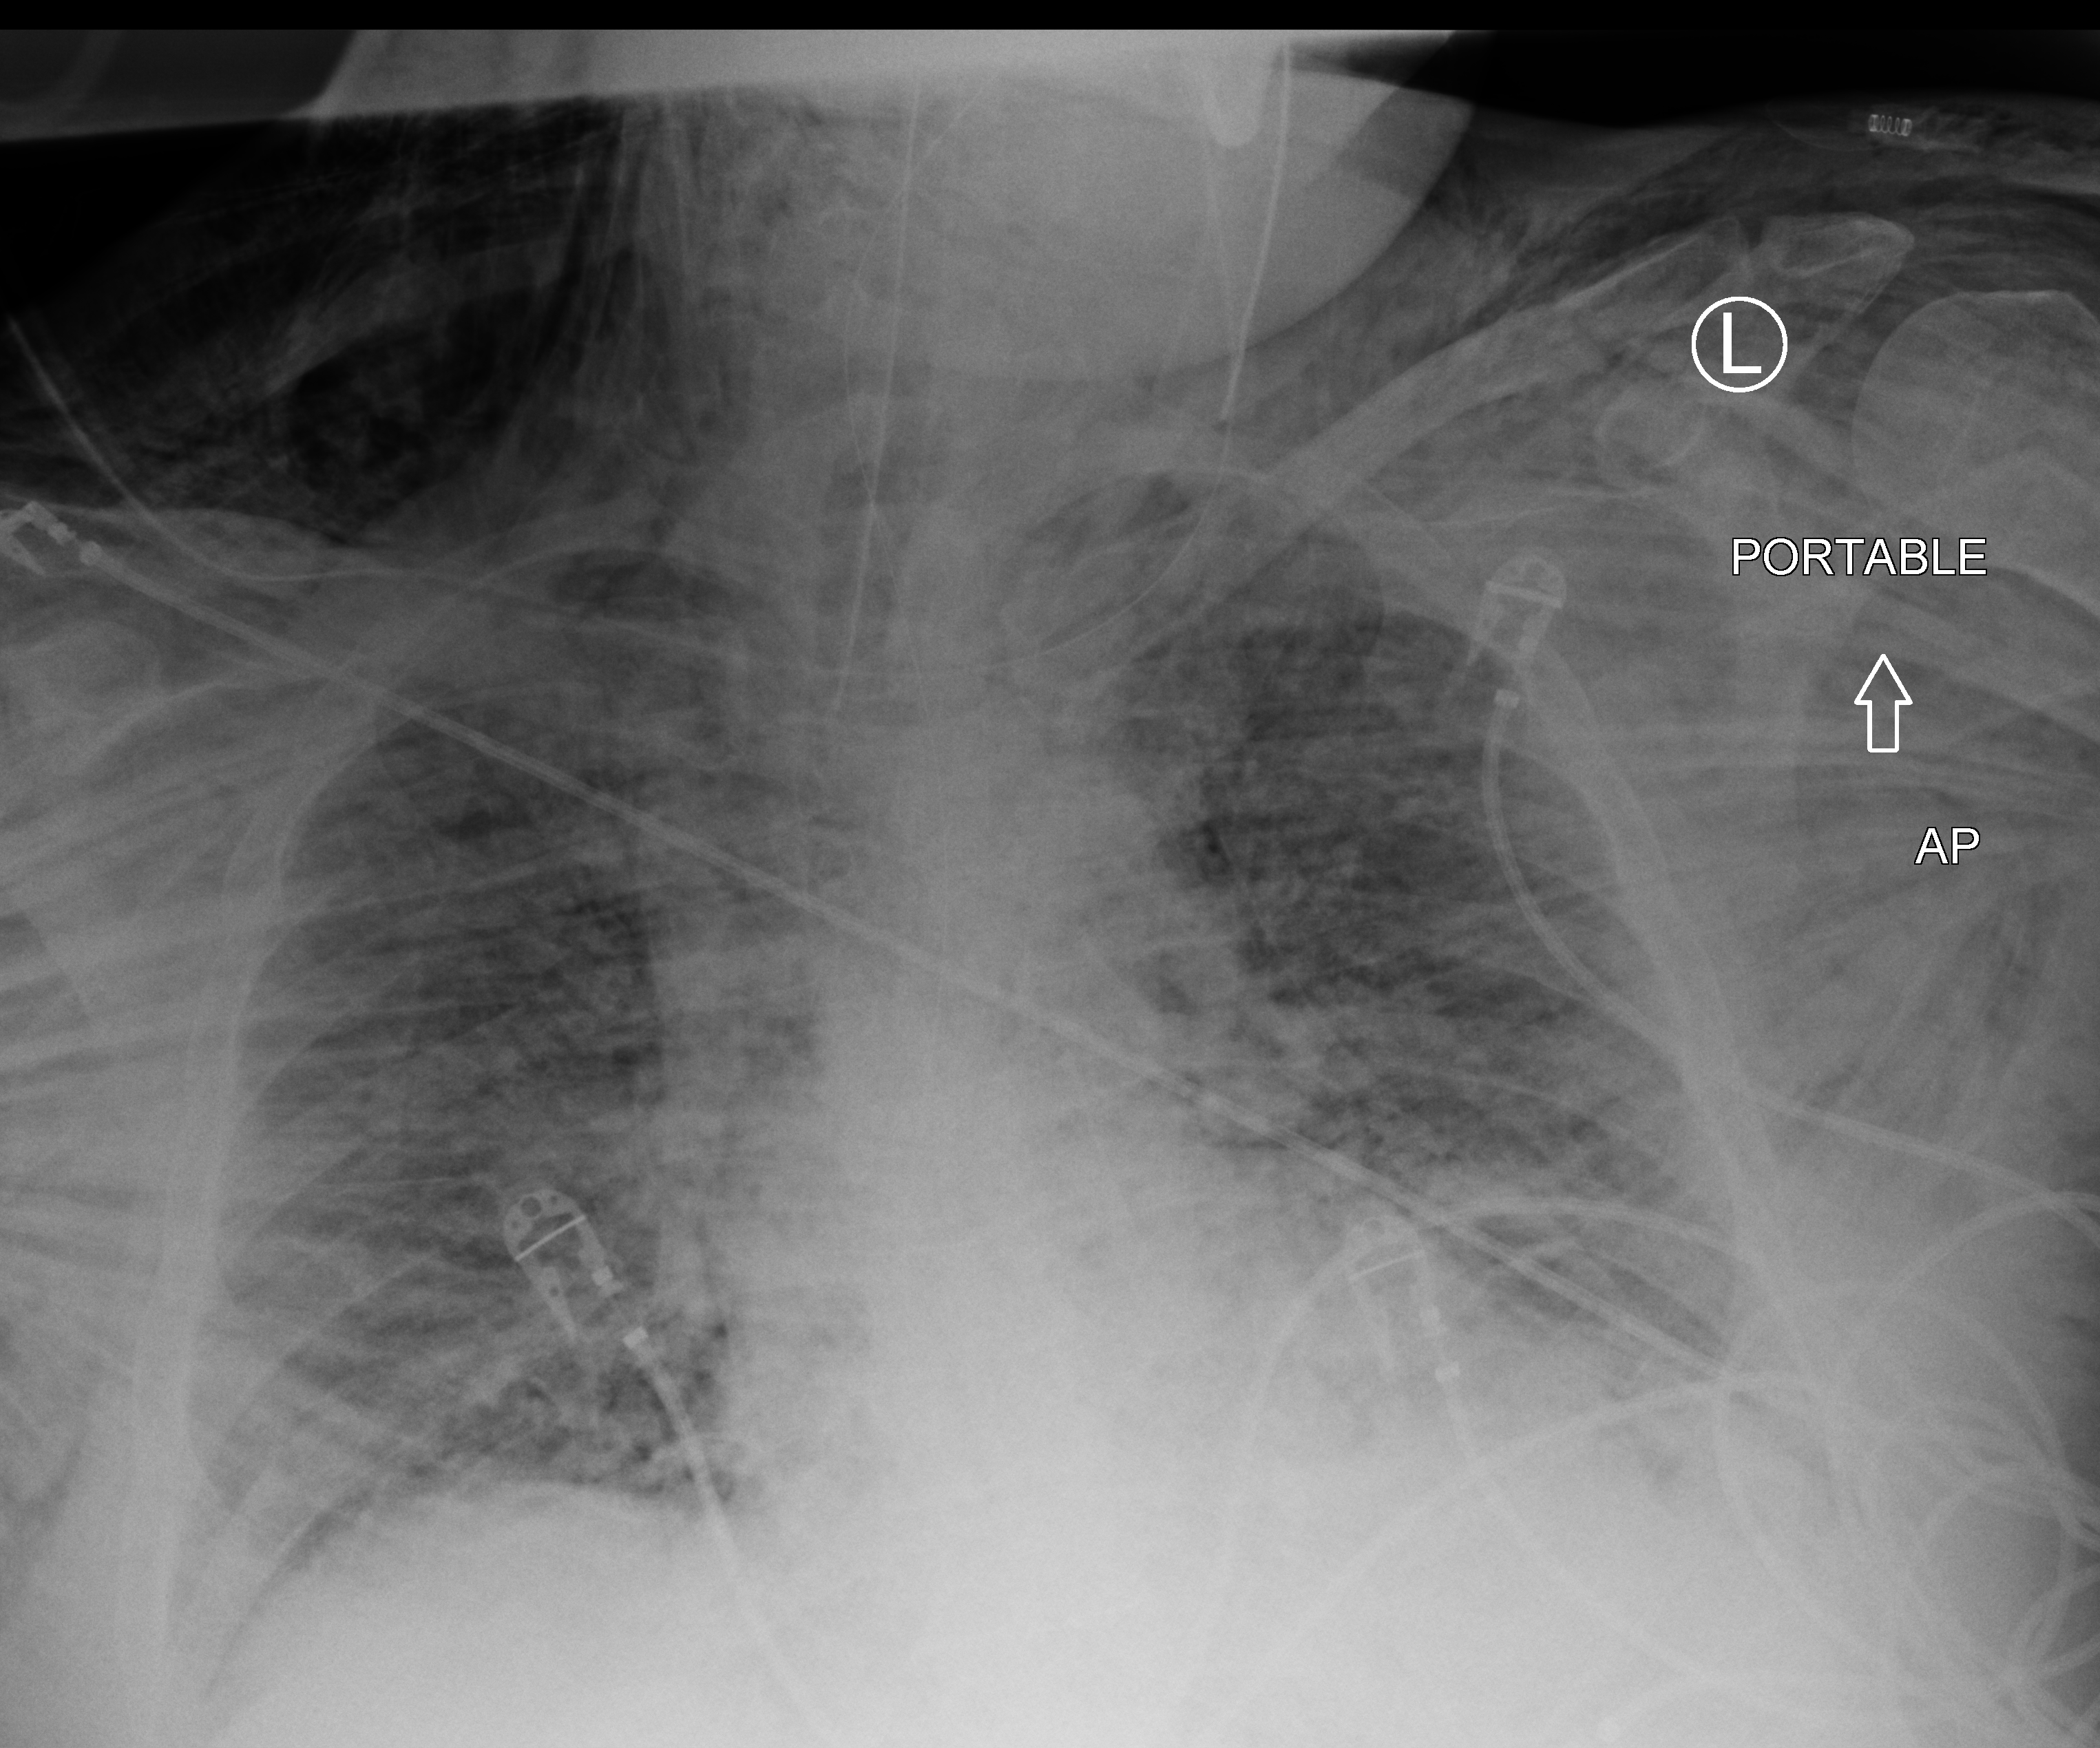
Bedside chest radiograph (computed radiography); anteroposterior (AP) projection. Adult patient hospitalised with COVID-19, age 18–59 years.
Admission-level facts for this patient (not findings on this image; timing relative to this image not recorded):
- admitted to intensive care during this hospital stay: yes
- mechanically ventilated during this hospital stay: yes